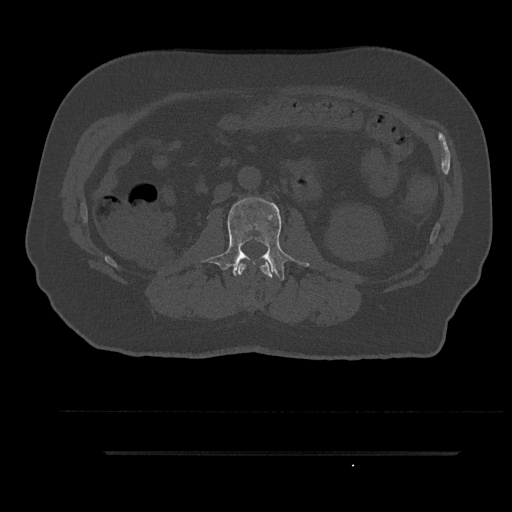
CT including the spine, one axial slice; position 116 of 797 along the scan axis; bone window (W 1800 / L 400 HU); 0.5 mm slice thickness; 512 × 512 image matrix, field of view 432 × 432 mm. Male patient, age 63 years. Case-level facts recorded for this patient, not image findings: primary cancer: renal.
Outlined on this slice (semi-automatic segmentation, software-assisted and operator-edited):
- L1 vertebra: bounding box (x1, y1, x2, y2) in pixels: (238, 259, 273, 278)
- L2 vertebra: (201, 197, 309, 281)